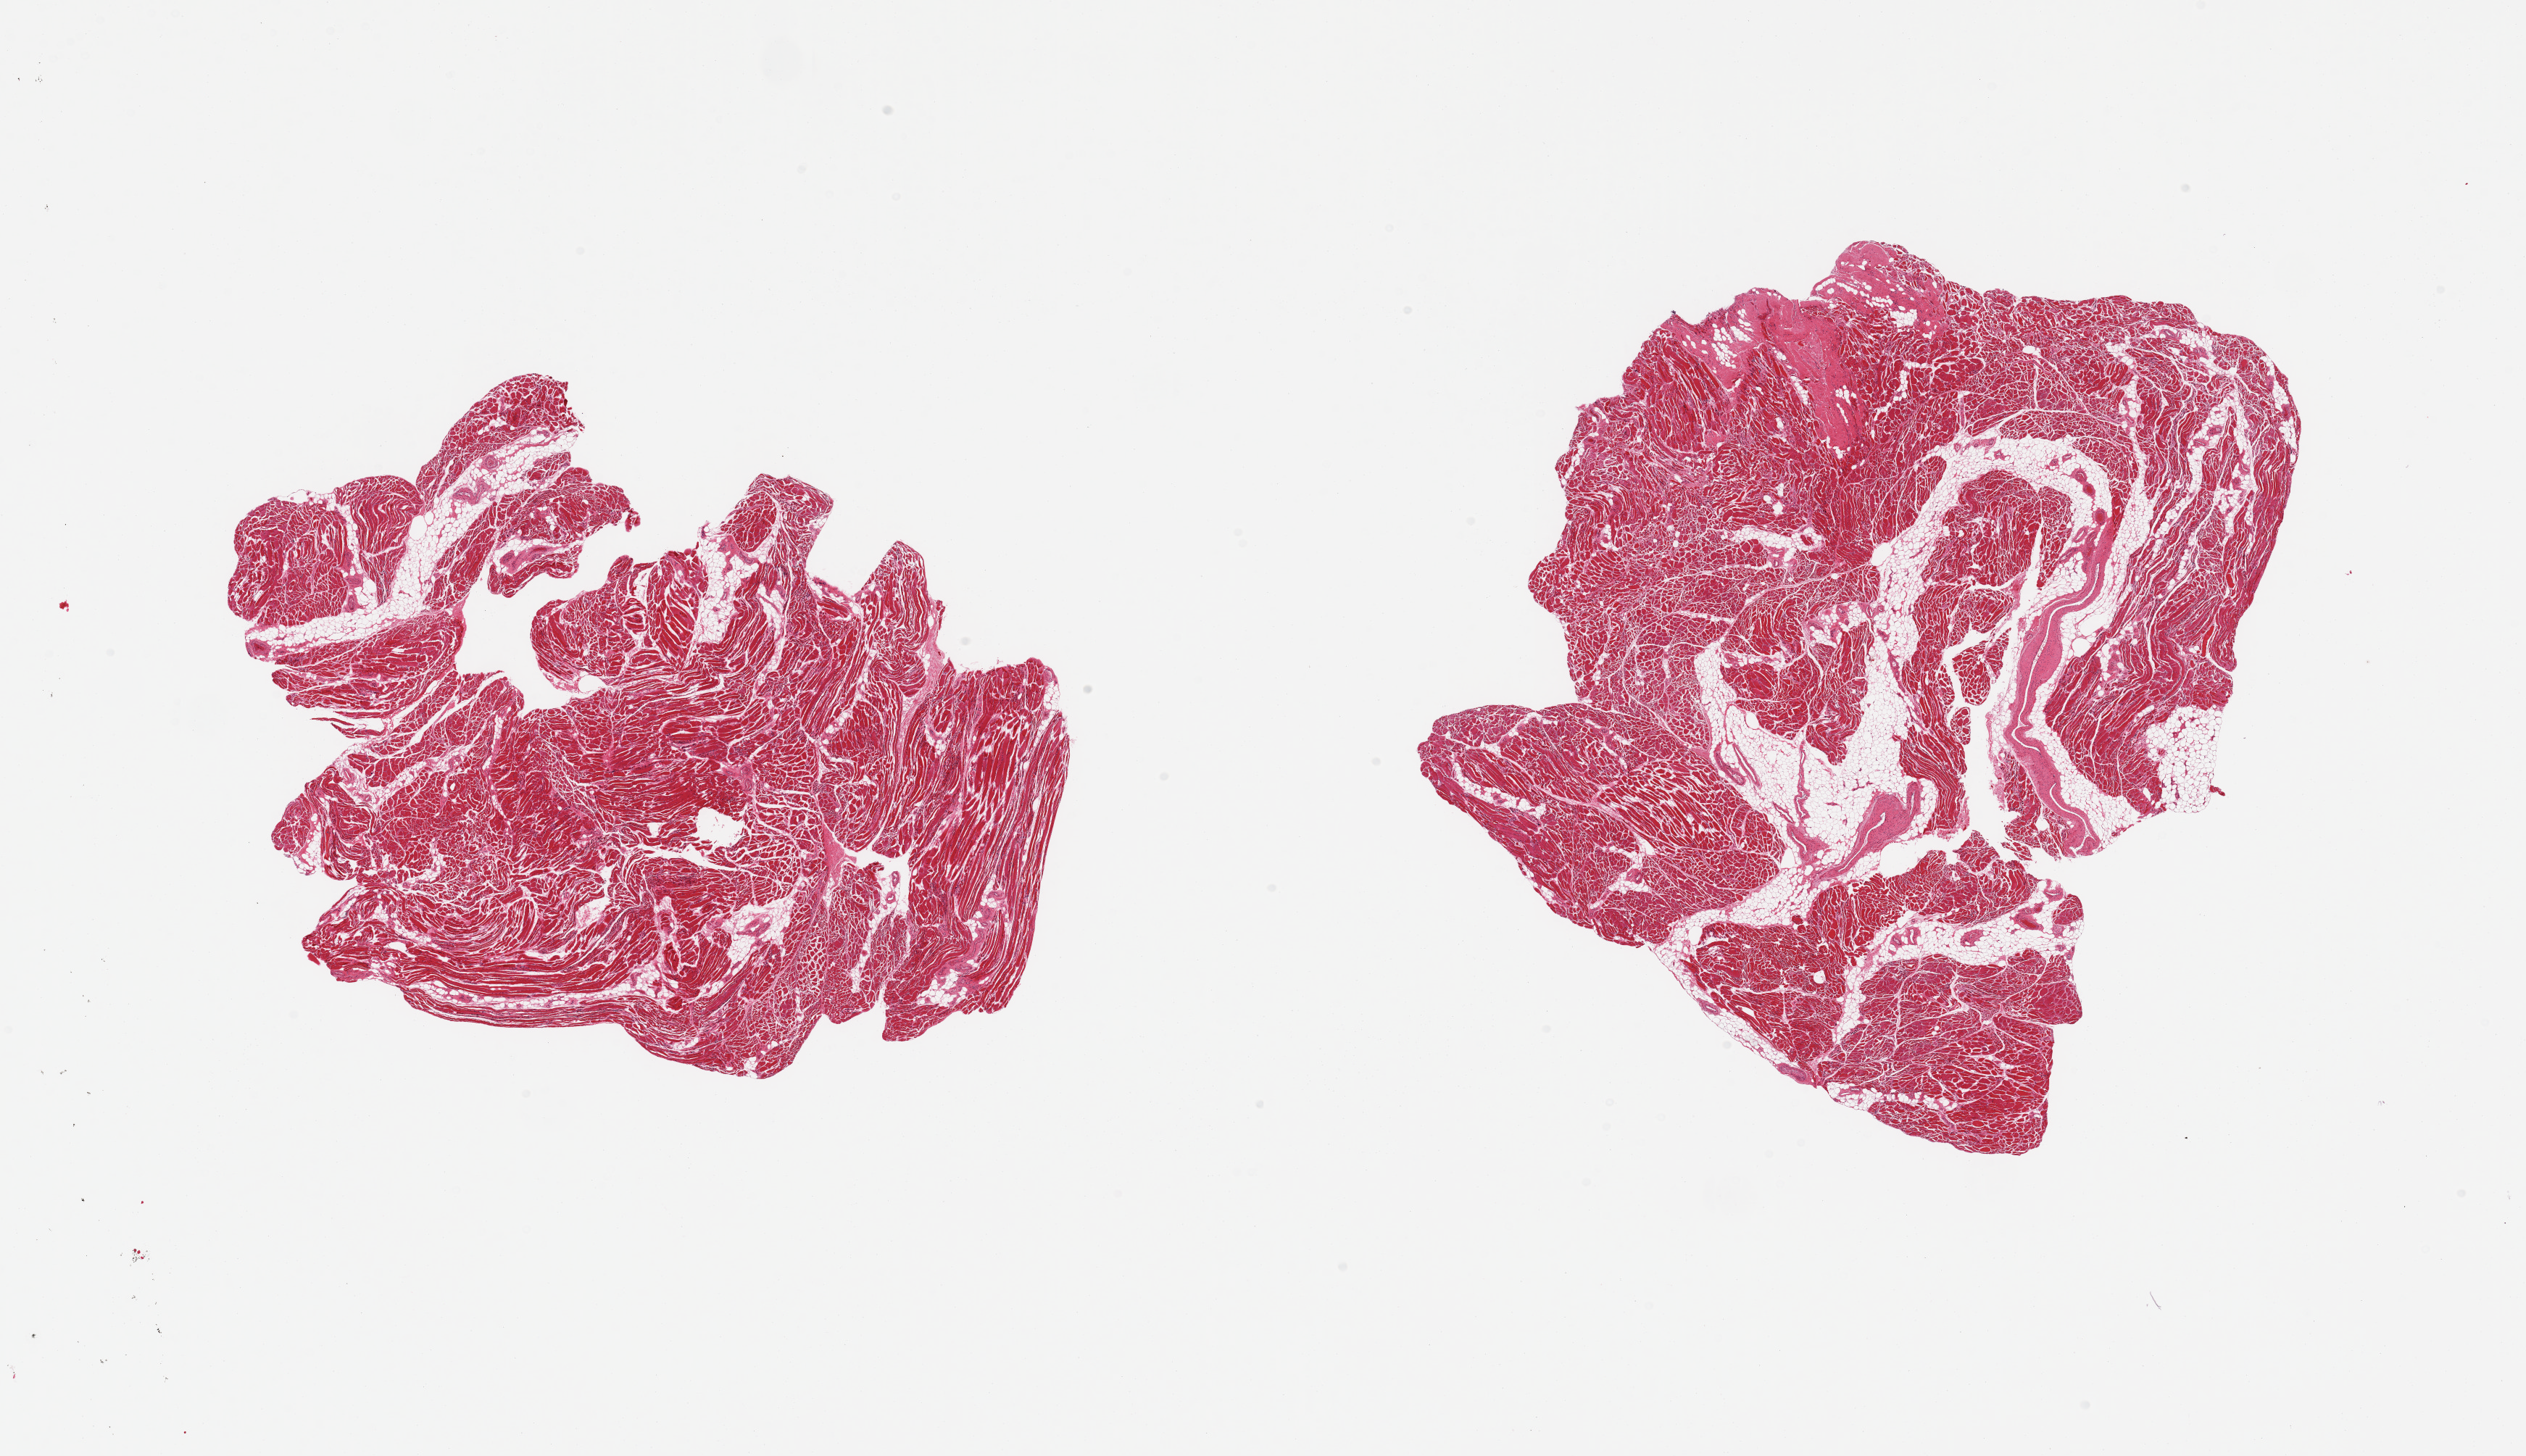
Whole-slide image, H&E stain, brightfield — a low-resolution overview of the entire scanned area, about 27.6 x 15.9 mm. PAXgene-fixed, paraffin-embedded tissue. Sampled site (target tissue): skeletal muscle. Tissue donor sample. Donor: female.
Pathologist's review note for this sample: 2 pieces, ~15-20% interstitial fat.